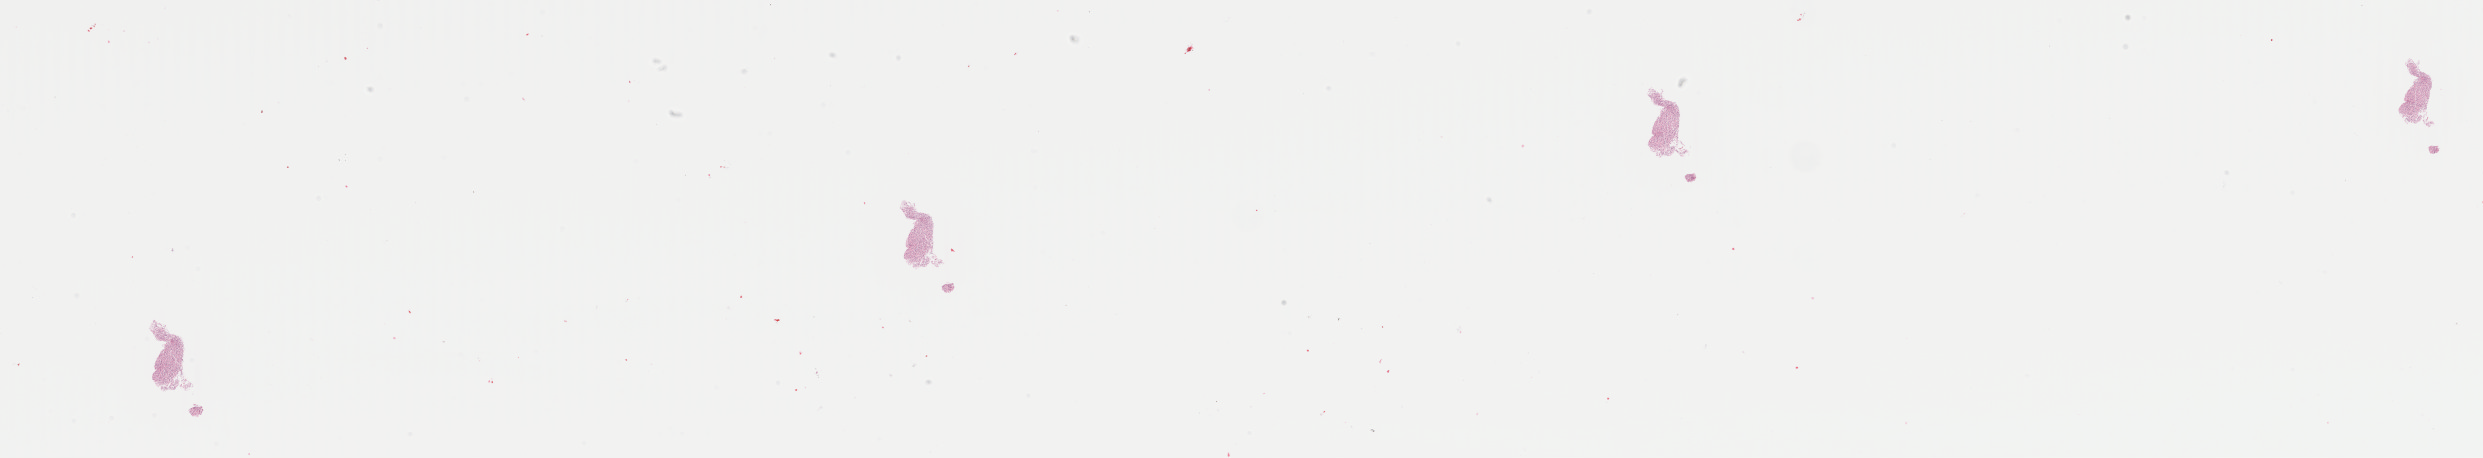
Digitized H&E tissue section (whole slide) — a low-resolution overview of the entire scanned area, about 39.5 x 7.3 mm (acquisition: 40x scan). Frozen section. Brain, primary tumour sample. Female patient; age at initial diagnosis 54 years. Histologic grade: G3 (poorly differentiated). Slide review estimates, as recorded: tumour cells 75%, tumour nuclei 95%, normal cells 5%, stromal cells 20%, necrosis 0%. Infiltration values recorded for this section: lymphocyte infiltration 0%, monocyte infiltration 0%, neutrophil infiltration 0%.
Pathologic diagnosis: Oligodendroglioma, anaplastic (cerebrum). Laterality: right.